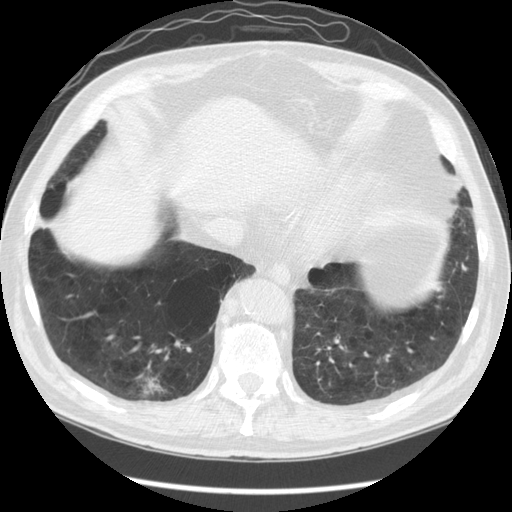
Low-dose screening chest CT, one axial slice. 120 kVp. Lung window (W 1500 / L -600 HU). 2.5 mm slice thickness. 512 × 512 image matrix, field of view 370 × 370 mm.
Structures marked on this image (manually delineated by an expert):
- lesion 1 (tumor, lower lobe of right lung): bounding box [x1, y1, x2, y2] px = [144, 378, 164, 395]